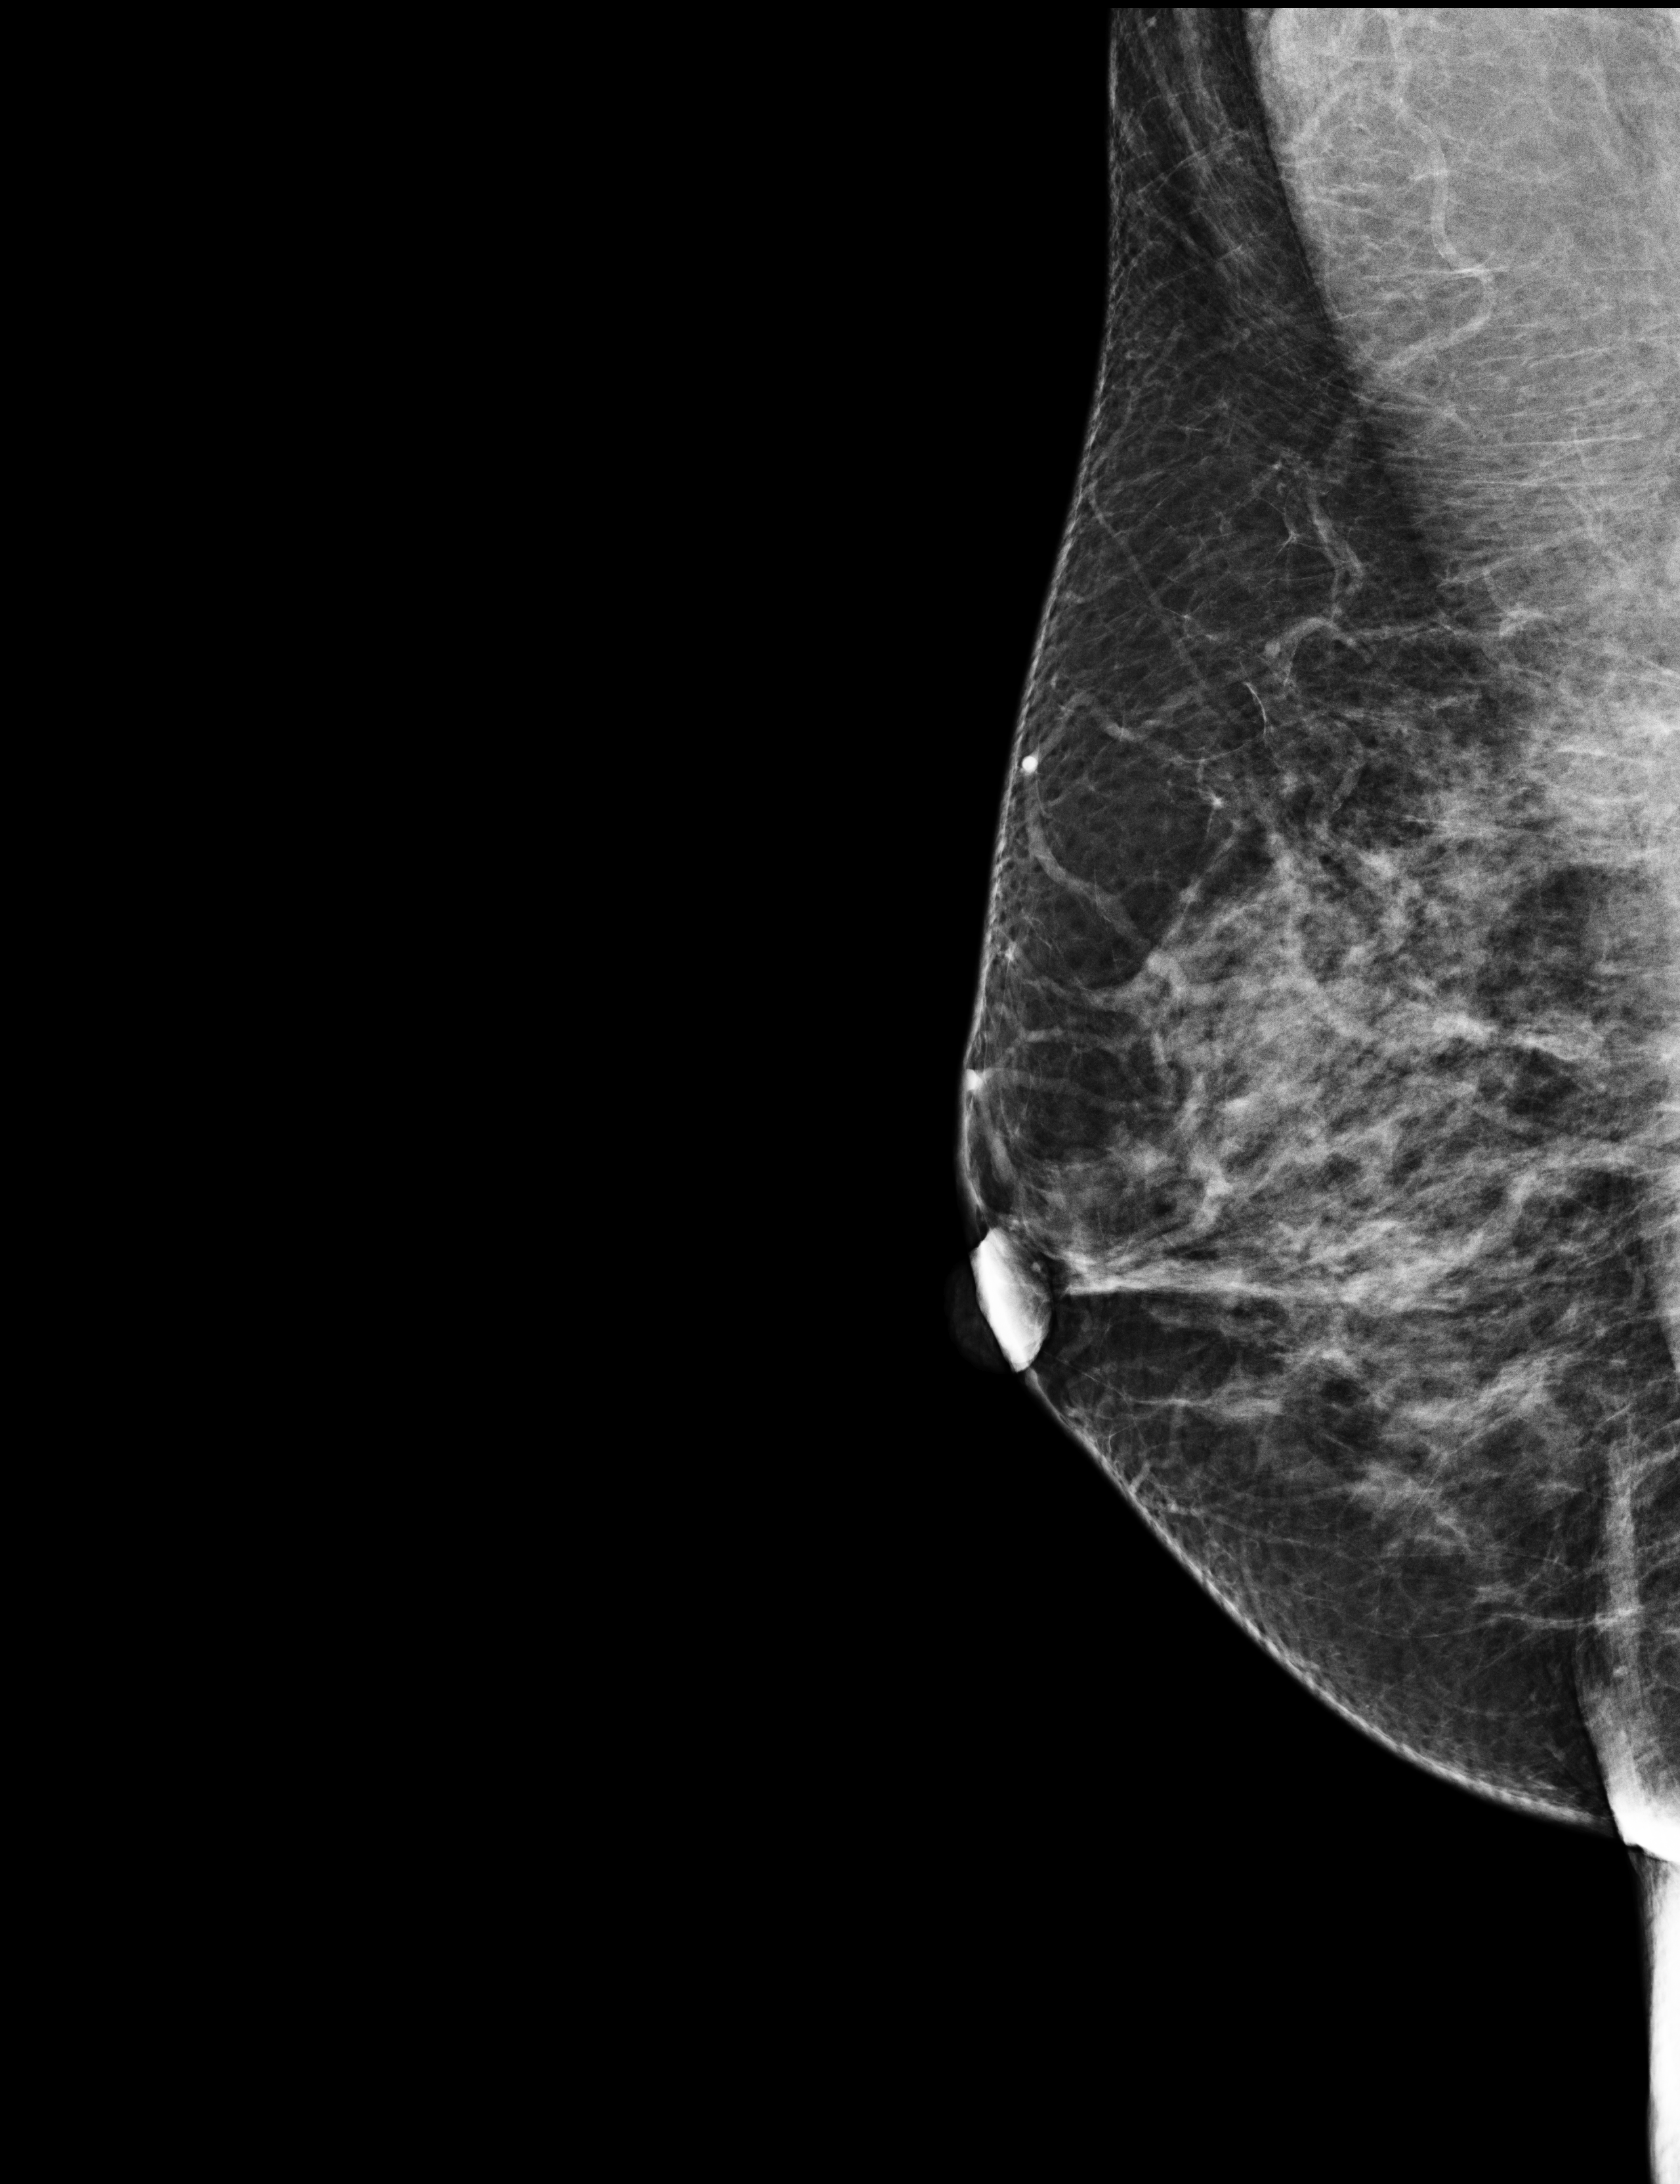
Annual screening mammography examination; compressed breast thickness 54 mm; system: Selenia Dimensions. Female patient, age 62 years.
Image type: full-field digital mammogram. Breast: right. Projection: medio-lateral oblique projection.